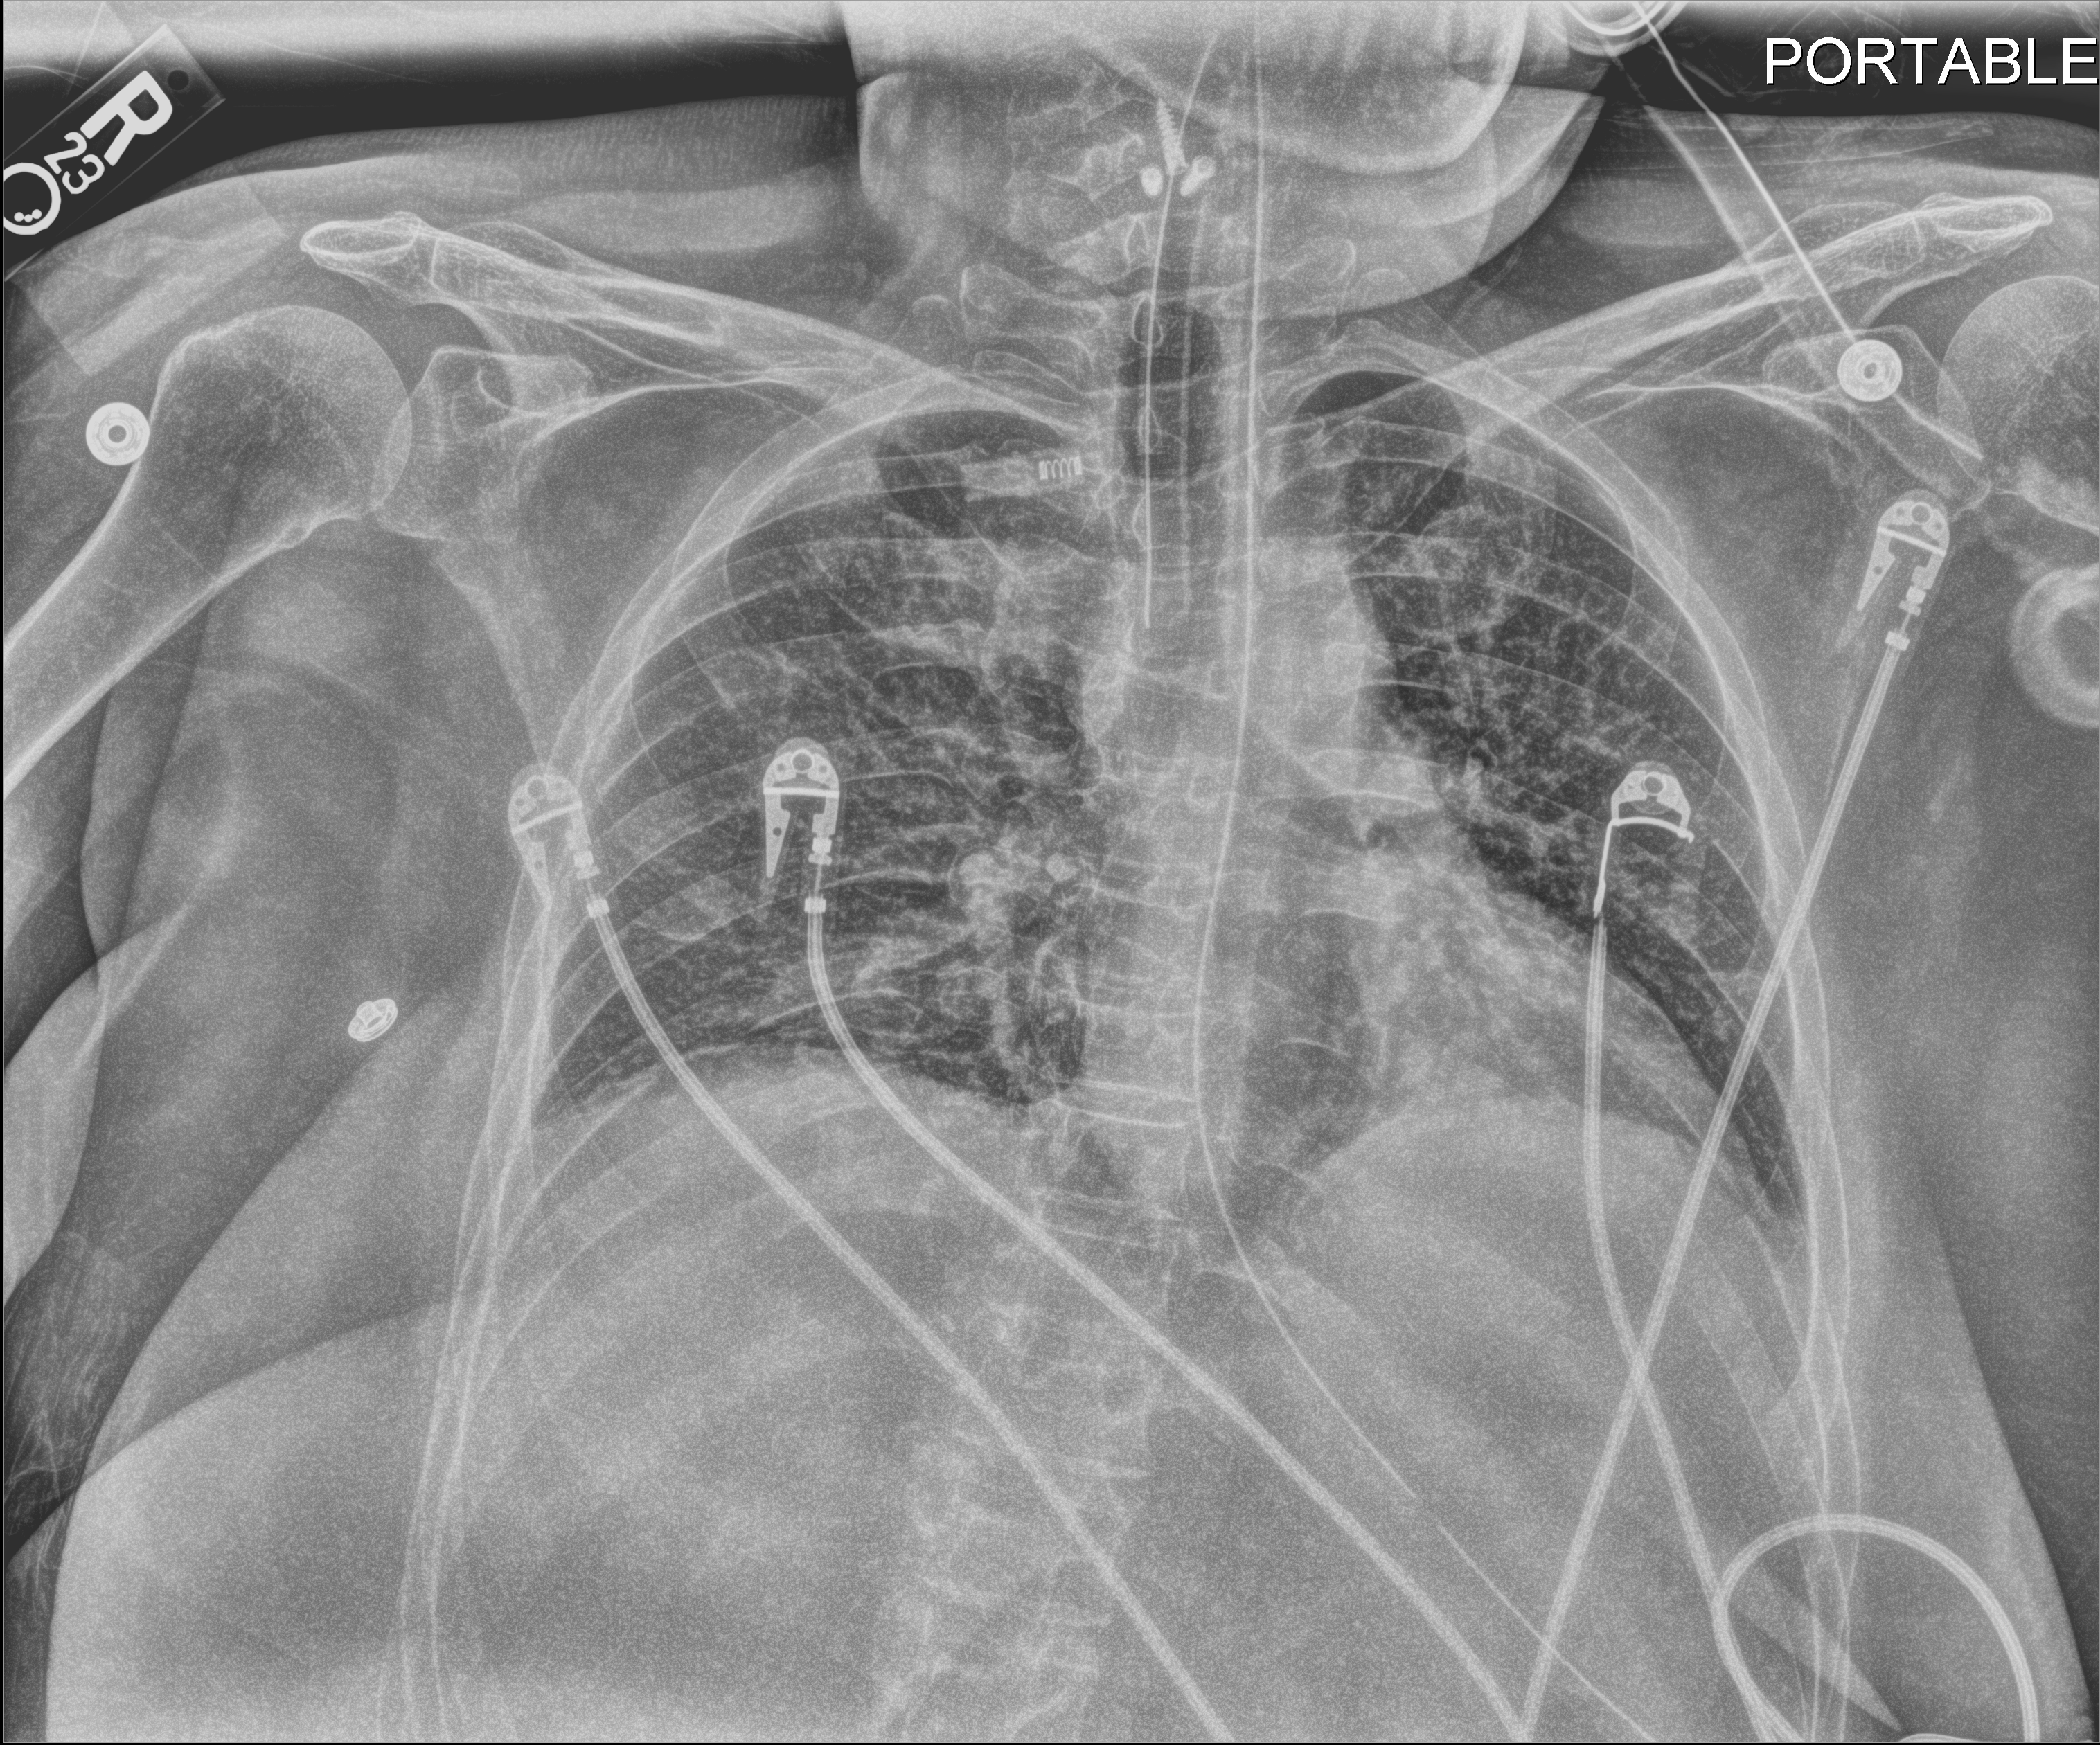
Bedside chest radiograph (digital radiography); anteroposterior (AP) projection. Patient hospitalised with COVID-19; female, aged 18–59 years.
Hospital-stay facts (about this admission, not read from this image; timing relative to this image not recorded):
- mechanically ventilated during this hospital stay: no